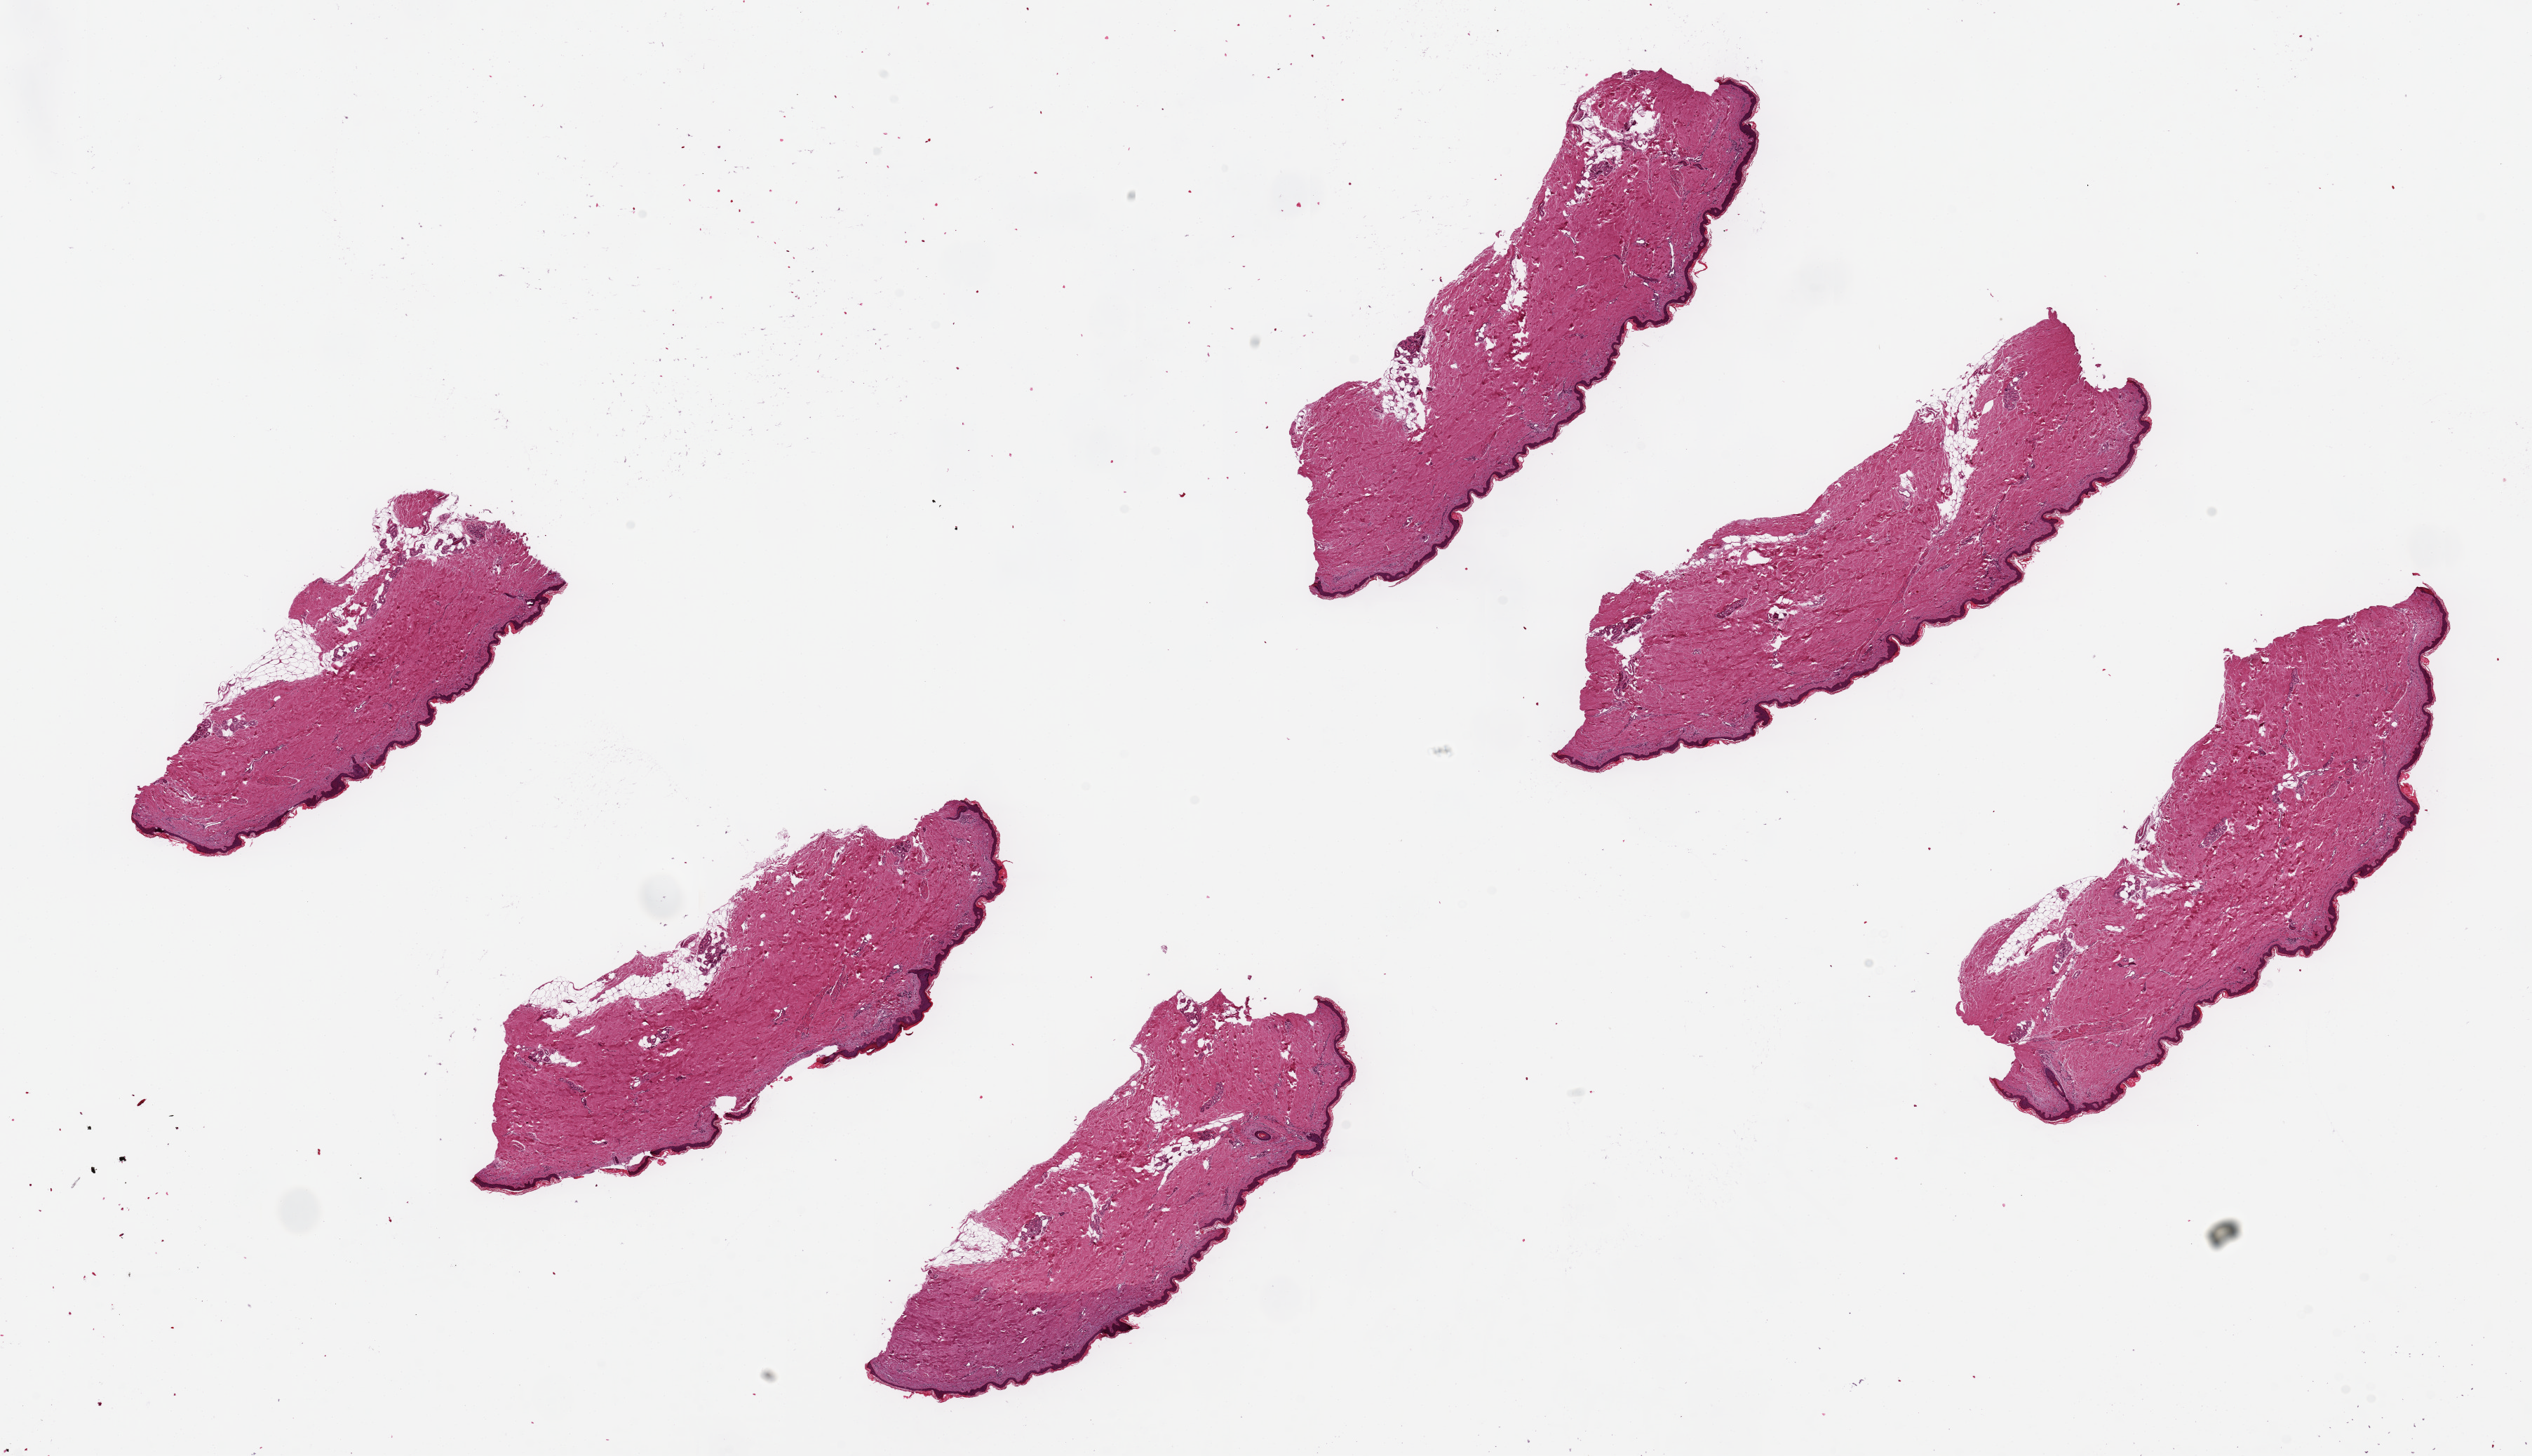
Haematoxylin and eosin whole-slide image, a low-resolution overview of the entire scanned area, about 28.5 x 16.4 mm (acquisition: 20x scan). PAXgene-fixed paraffin-embedded (PFPE) section. Section of skin of lower leg (target tissue). Tissue donor sample.
Review note (as recorded): 6 pieces, ~6.5x2mm. Squamous epithelium is ~2% of thickness.